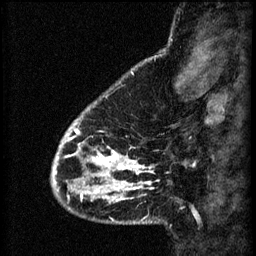
Breast MRI (dynamic contrast-enhanced), one sagittal slice; position 12 of 60 along the scan axis; 3 images stored at this slice position (order not interpretable as contrast timing); 1.5 T; TE 4.2 ms, TR 8.2 ms; 2.2 mm slice thickness; 256 × 256 image matrix, field of view 180 × 180 mm. Female patient, age 41 years.
Structures marked on this image (semi-automatic segmentation, software-assisted and operator-edited):
- analysis volume of interest (the breast-tissue region the enhancement analysis was run in; not a lesion): bounding box [x1, y1, x2, y2] px = [56, 104, 157, 207]
- tumour enhancement mask (voxels above the 70 % enhancement threshold inside the analysis volume of interest): [56, 118, 153, 203]